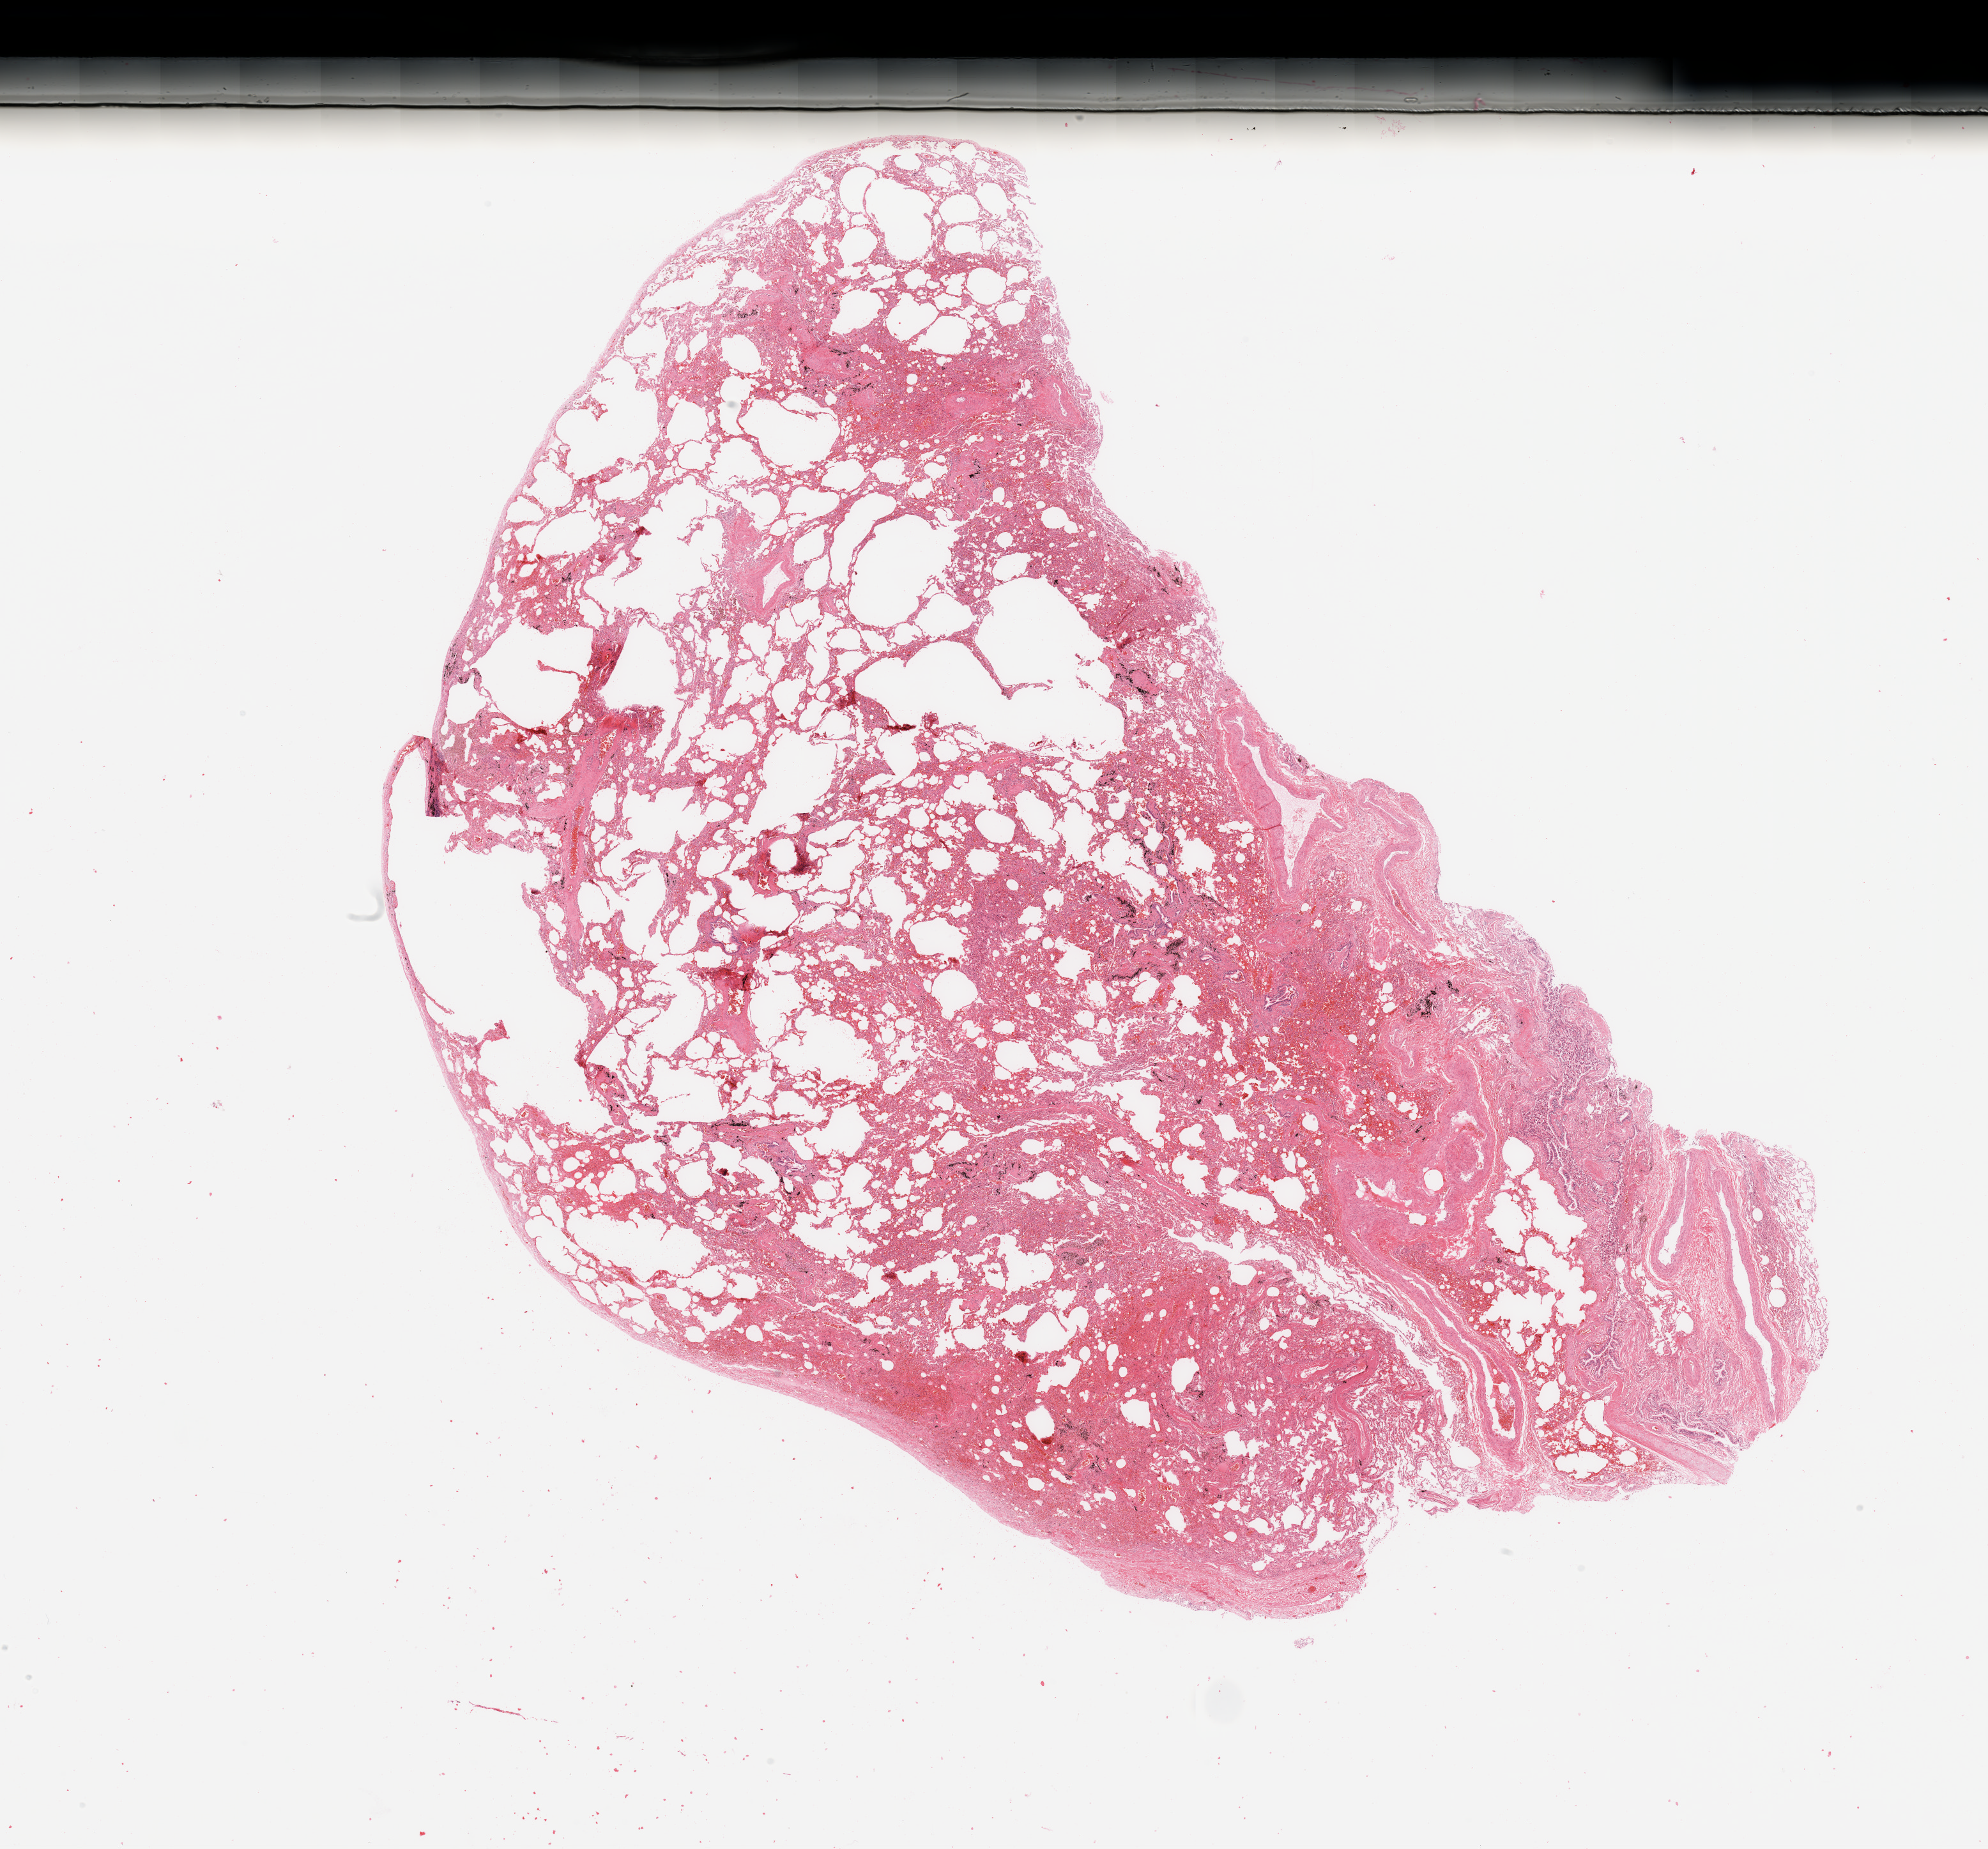
Whole-slide histology image, Hematoxylin and eosin (H&E) stained, whole scanned area (about 24.6 x 22.9 mm) shown as a low-resolution overview. Normal (non-tumour) tissue sample, sampled site: lung. Male, 58 y/o.
* this section: normal (non-tumour) tissue from the same patient
* patient diagnosis: Adenocarcinoma, NOS